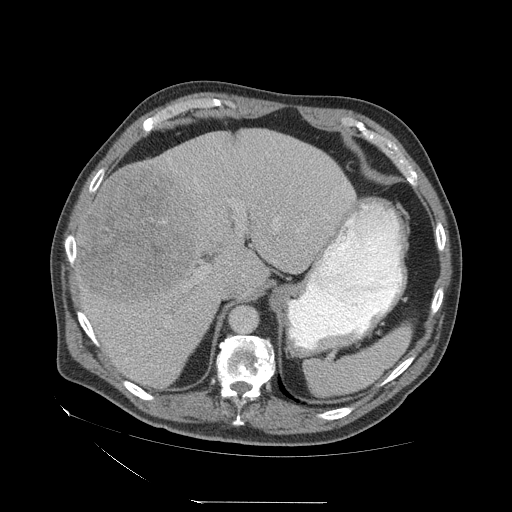
Contrast-enhanced abdominal CT (liver protocol), one axial slice; position 45 of 83 along the scan axis; reconstruction kernel STANDARD; 140 kVp; soft-tissue window (W 400 / L 40 HU); 2.5 mm slice thickness; 512 × 512 image matrix, field of view 460 × 460 mm. Case-level facts recorded for this patient, not image findings: diagnosis: hepatocellular carcinoma (patient treated with transarterial chemoembolisation; whether this scan precedes or follows treatment is not stated here); TNM stage (as recorded): Stage-I; Child-Pugh class: A; tumour differentiation: well differentiated; tumour nodularity: uninodular.
Annotated regions visible in this slice (semi-automatic segmentation, software-assisted and operator-edited):
- liver parenchyma outside the tumour (the mass and vessels are separate outlines, so this box may not span the whole liver): bounding box [x1, y1, x2, y2] px = [76, 128, 354, 388]
- mass: [81, 165, 203, 308]
- liver vessels: [87, 182, 346, 344]